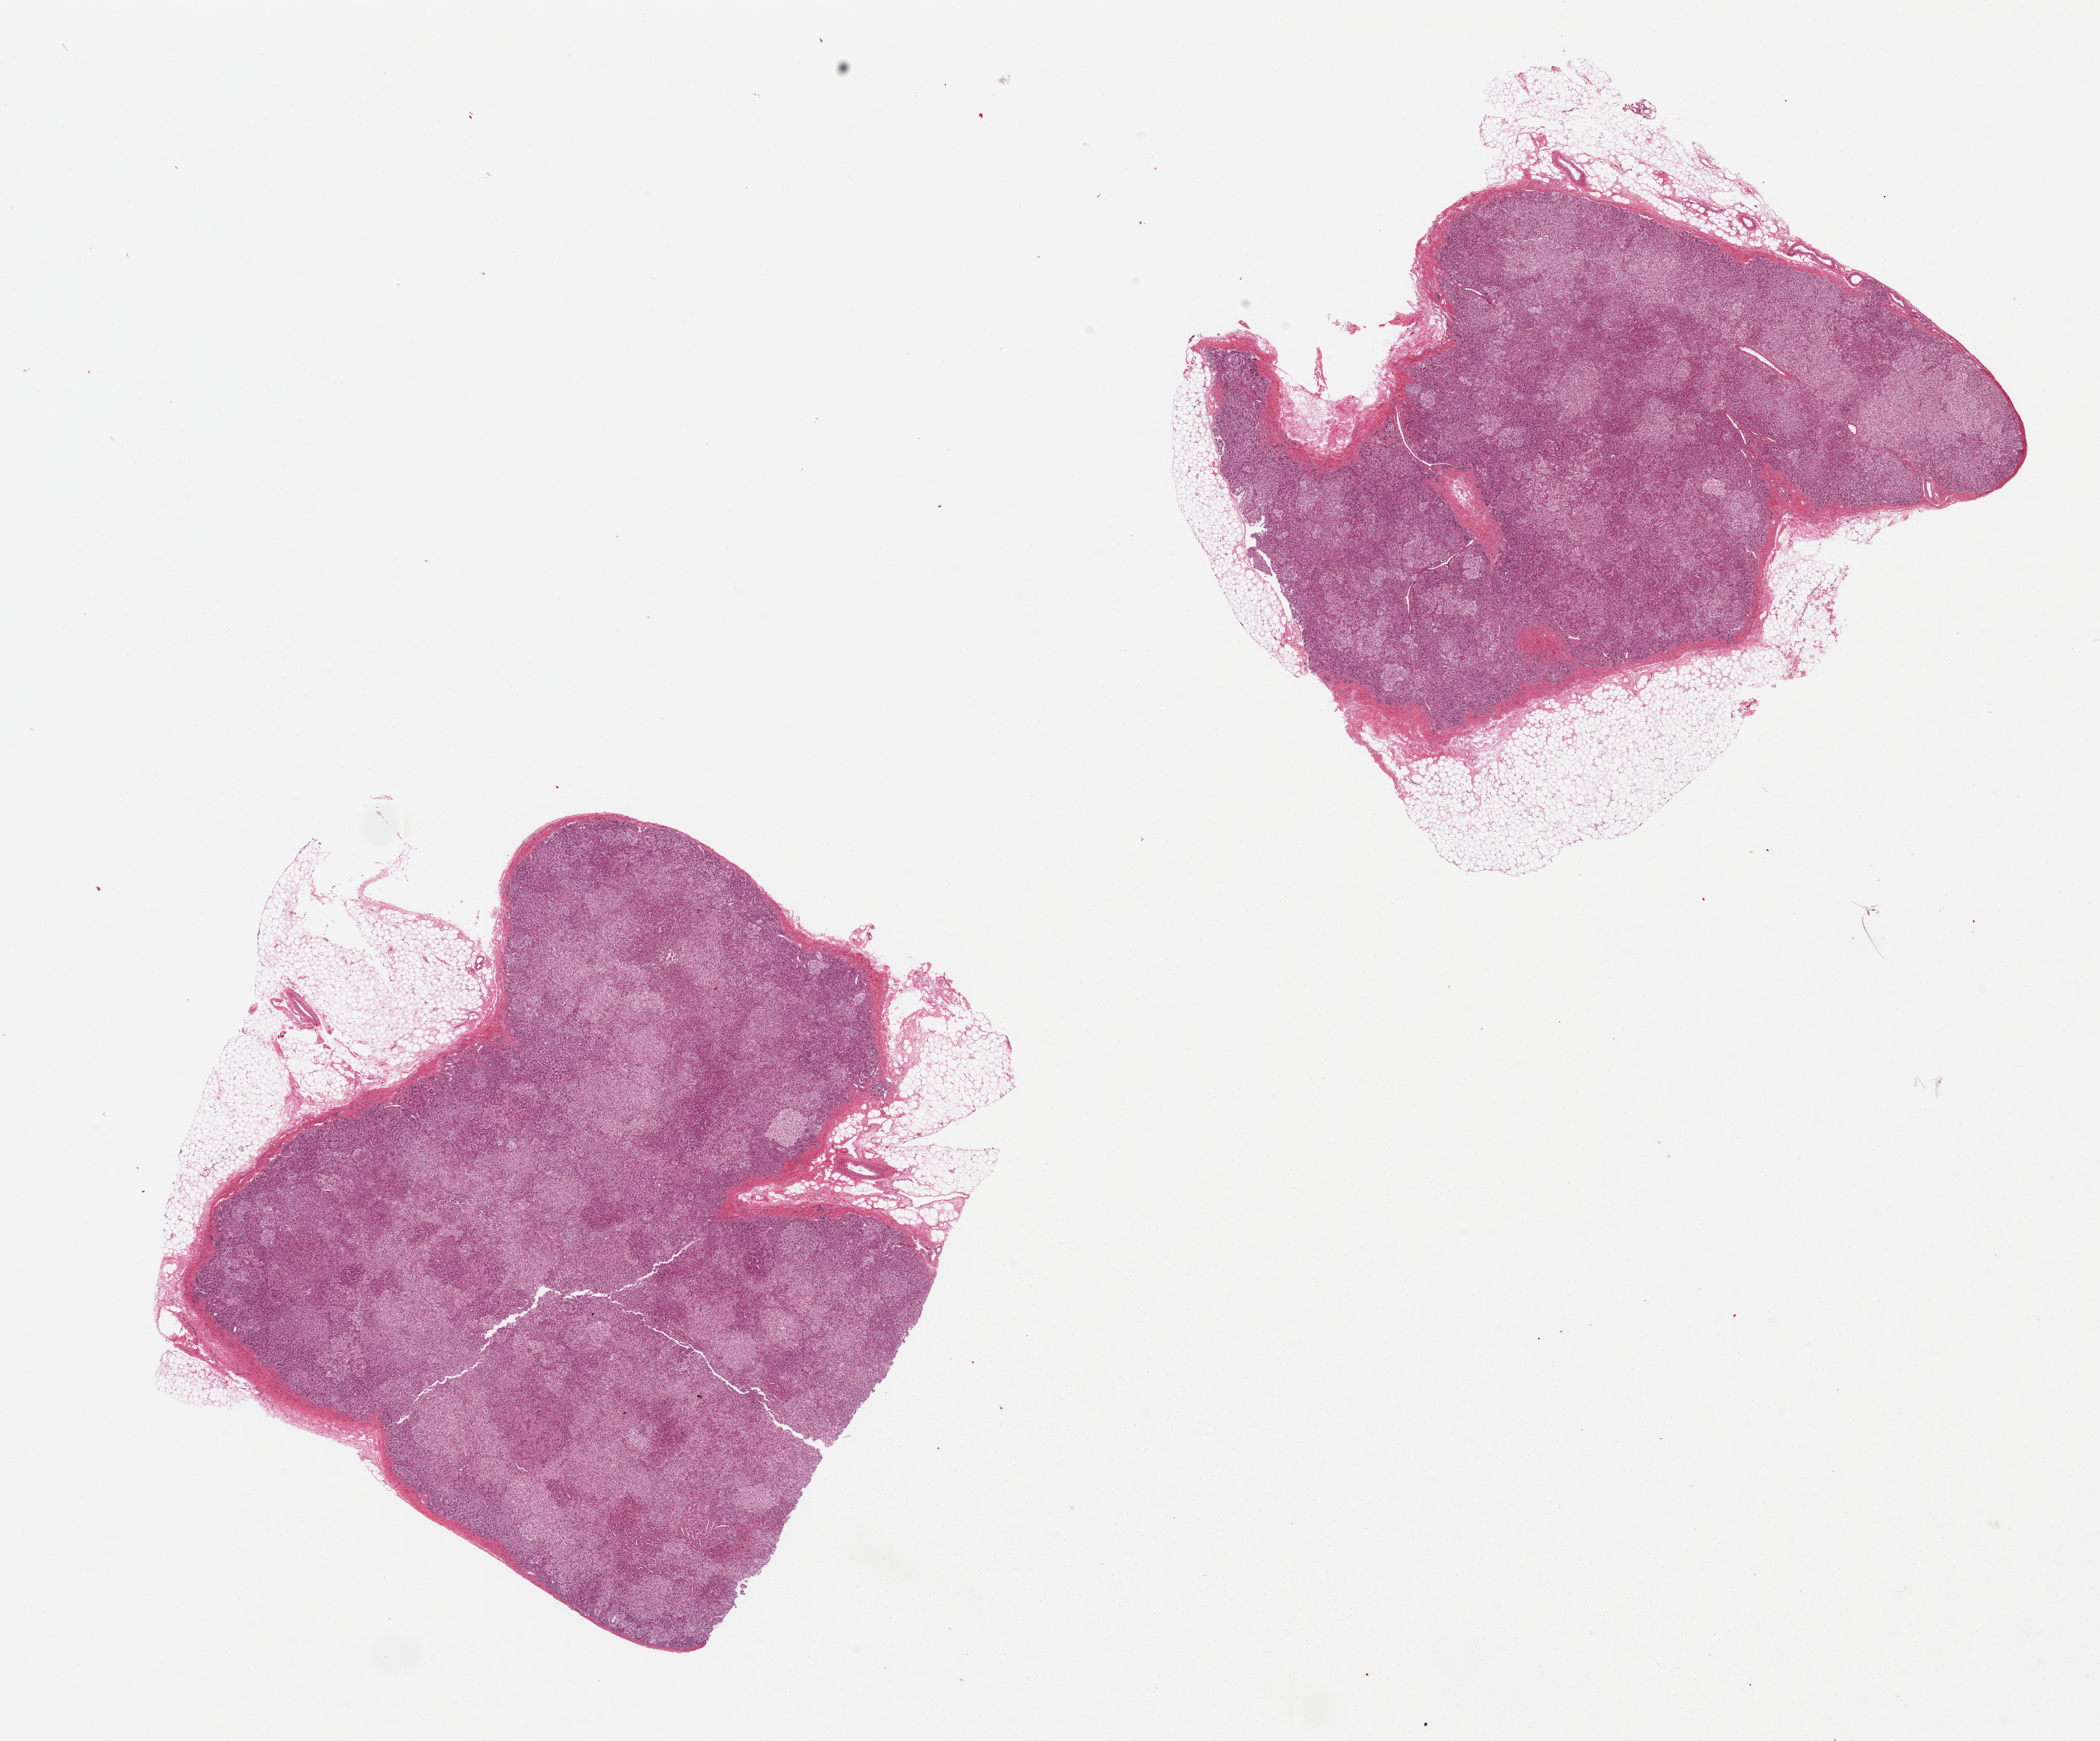
Haematoxylin and eosin whole-slide image — whole scanned area (about 25.6 x 21.2 mm) shown as a low-resolution overview. PAXgene-fixed, paraffin-embedded tissue. Target tissue: adrenal gland. Donor tissue sample. Donor: female.
* review note (as recorded): 2 pieces